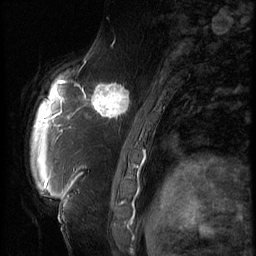
Breast MRI (dynamic contrast-enhanced), one sagittal slice; 3 images stored at this slice position (order not interpretable as contrast timing); 1.5 T; TE 4.2 ms, TR 9 ms; 2.5 mm slice thickness; 256 × 256 image matrix, field of view 180 × 180 mm. Patient: female, 57 years. From the clinical record (not read from this slice): setting: breast cancer imaged before/during neoadjuvant chemotherapy; receptor status: triple-negative.
Structures marked on this image (semi-automatic segmentation, software-assisted and operator-edited):
- analysis volume of interest (the breast-tissue region the enhancement analysis was run in; not a lesion): bounding box (x1, y1, x2, y2) in pixels: (86, 74, 138, 129)
- tumour enhancement mask (voxels above the 140 % enhancement threshold inside the analysis volume of interest): (86, 81, 132, 120)